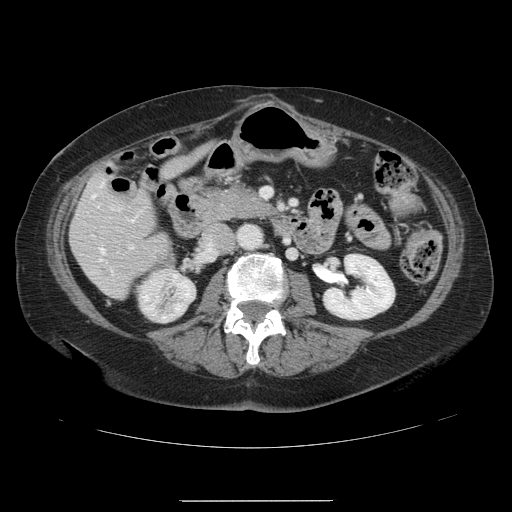
Contrast-enhanced abdominal CT, one axial slice; slice 42 of 141 in the series (ordered by position); intravenous contrast given; soft-tissue window (W 400 / L 40 HU); 512 × 512 image matrix, field of view 393 × 393 mm. Female patient, age 74 years. Case-level facts recorded for this patient, not image findings: diagnosis: colorectal cancer liver metastases, imaged before liver resection; multiple liver metastases: yes; largest metastasis: 7 cm; chemotherapy before resection: no.
Structures marked on this image (outlined manually by an expert reader):
- hepatic veins: bounding box <92,182,132,253> (left, top, right, bottom; pixels)
- liver: <71,177,170,297>
- planned liver remnant (the part of the liver to remain after resection): <71,192,170,290>
- portal vein (with intrahepatic branches): <111,207,133,248>